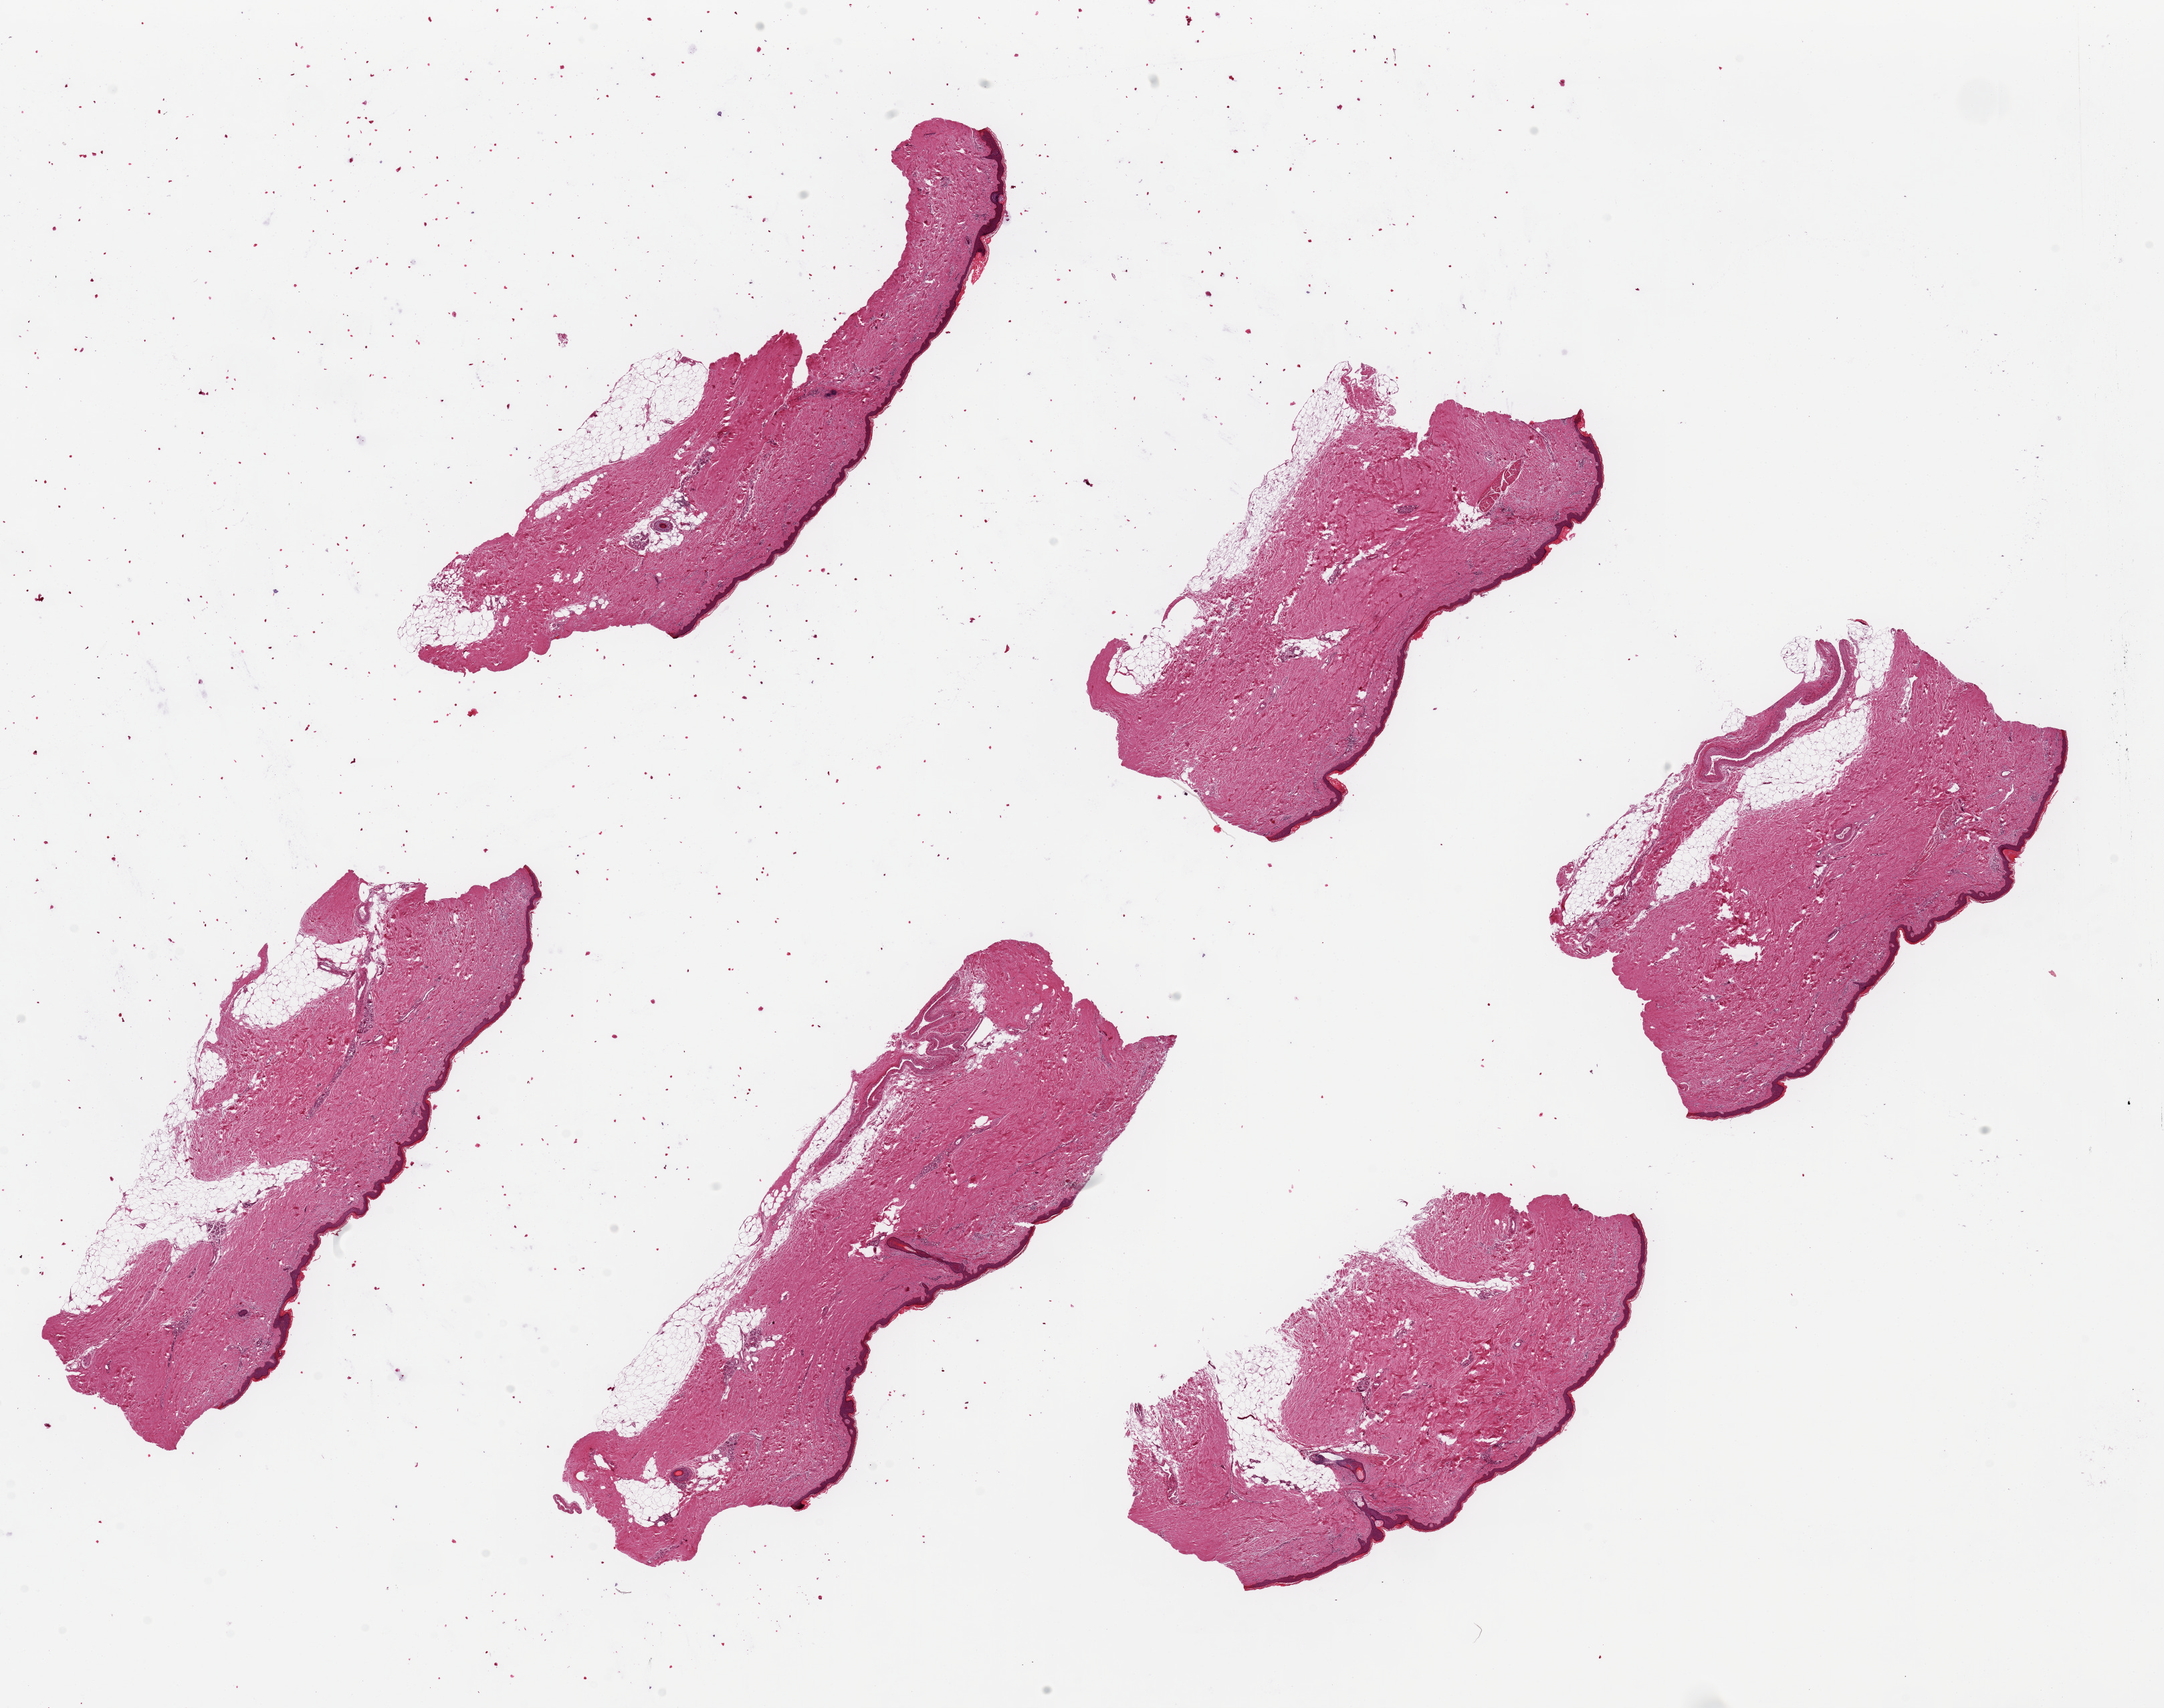
Whole-slide image, haematoxylin and eosin stain — shown as a low-resolution overview of the whole scanned area (about 25.6 x 20.2 mm); PAXgene-fixed, paraffin-embedded tissue; sampled site (target tissue): skin of lower leg; donor tissue sample. Donor sex: male.
Reviewer comment on this tissue sample: 6 pieces ~7x2.5mm. Squamous epithelium is 2-3% of thickness.